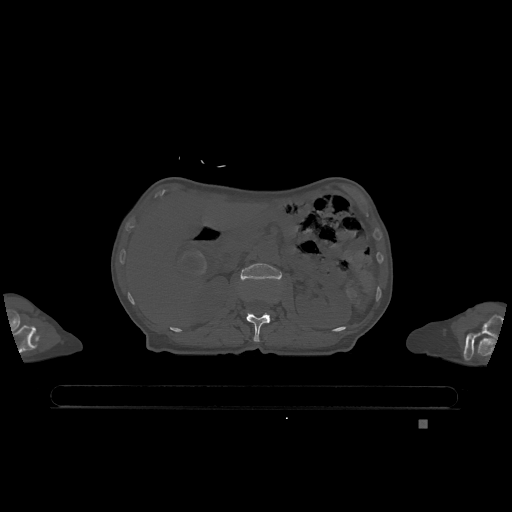
CT including the spine, one axial slice; bone window (W 1800 / L 400 HU); 0.5 mm slice thickness; 512 × 512 image matrix. Female patient, age 74 years. From the clinical record (not read from this slice): primary cancer: lung.
Annotated regions visible in this slice (semi-automatic segmentation, software-assisted and operator-edited):
- L1 vertebra: bounding box <246,313,270,342> (left, top, right, bottom; pixels)
- L2 vertebra: <241,263,282,280>